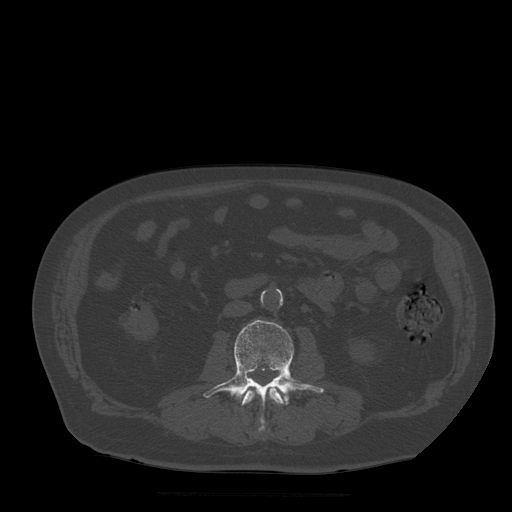
CT including the spine, one axial slice. Slice 144 of 522 in the series (ordered by position). Bone window (W 1800 / L 400 HU). 1.25 mm slice thickness. 512 × 512 image matrix, field of view 420 × 420 mm. Patient age 72 years. Case-level facts recorded for this patient, not image findings: primary cancer: prostate.
Outlined on this slice (semi-automatically segmented with operator editing):
- L2 vertebra: bounding box [x1, y1, x2, y2] px = [242, 383, 286, 432]
- L3 vertebra: [203, 320, 325, 422]